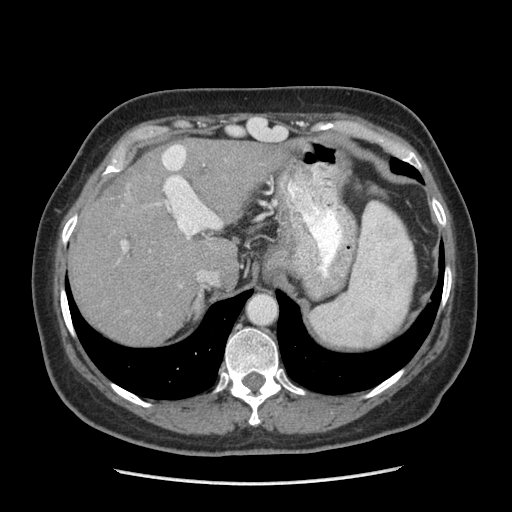
Contrast-enhanced abdominal CT (liver protocol), one axial slice; slice 161 of 185 in the series (ordered by position); 140 kVp; soft-tissue window (W 400 / L 40 HU); 2.5 mm slice thickness; 512 × 512 image matrix, field of view 360 × 360 mm. From the clinical record (not read from this slice): diagnosis: hepatocellular carcinoma (patient treated with transarterial chemoembolisation; whether this scan precedes or follows treatment is not stated here); TNM stage (as recorded): Stage-I; Child-Pugh class: A; tumour differentiation: poorly differentiated; tumour nodularity: uninodular.
Annotated regions visible in this slice (semi-automatically segmented with operator editing):
- abdominal aorta: bounding box (x1, y1, x2, y2) in pixels: (249, 296, 275, 323)
- liver parenchyma outside the tumour (the mass and vessels are separate outlines, so this box may not span the whole liver): (68, 139, 274, 344)
- mass: (123, 169, 166, 218)
- liver vessels: (121, 145, 221, 277)